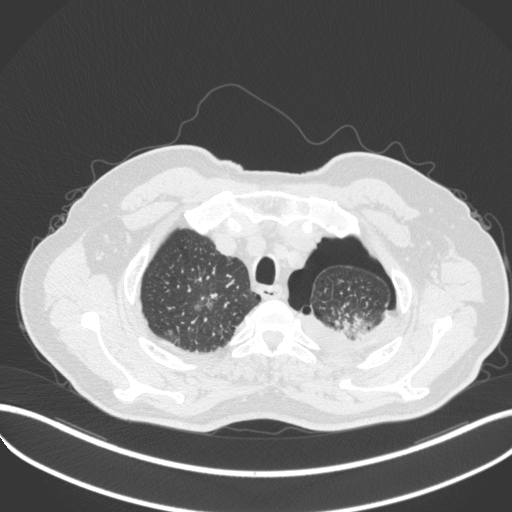
Chest CT, one axial slice. Position 427 of 466 along the scan axis. 120 kVp. Lung window (W 1500 / L -600 HU). 1 mm slice thickness. 512 × 512 image matrix, field of view 400 × 400 mm. Male patient, age 76 years. From the clinical record (not read from this slice): clinical TNM (as recorded): T3 N0 M1b.
Annotated regions visible in this slice (rectangle marked by the reading radiologist):
- lung tumour (recorded histology: adenocarcinoma): bounding box <333,311,370,342> (left, top, right, bottom; pixels)